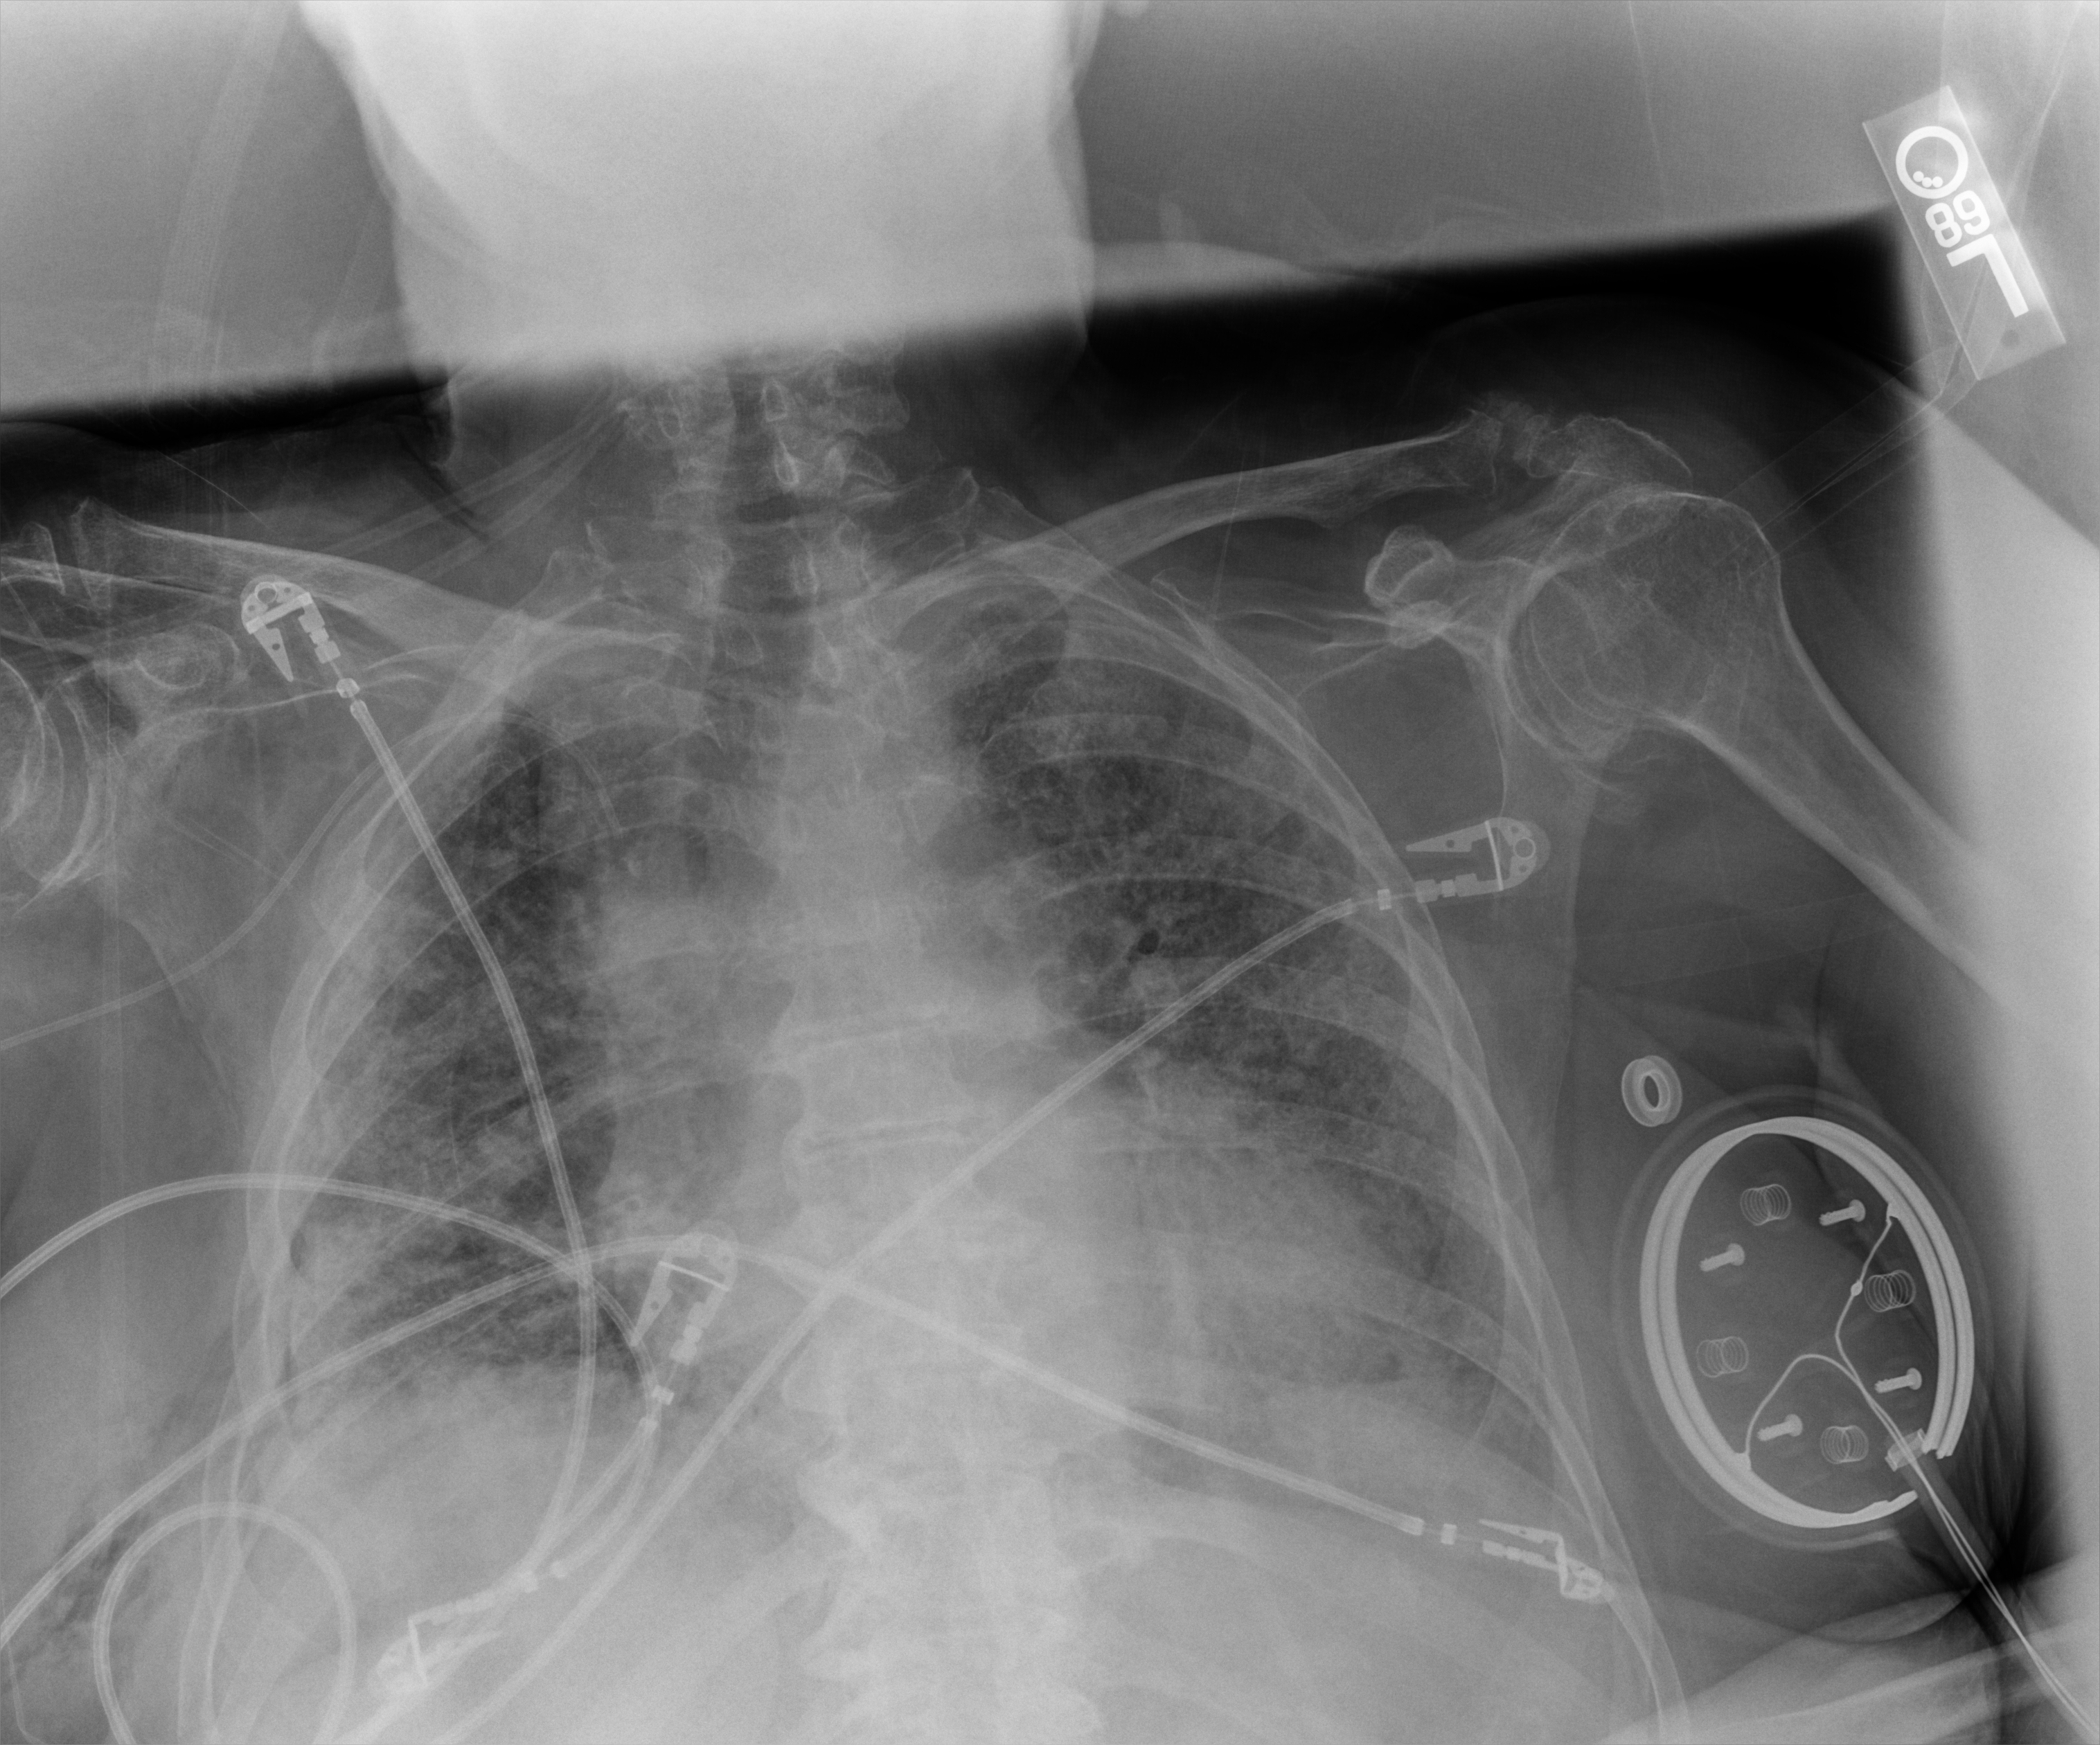
Bedside chest radiograph (digital radiography). Female patient hospitalised with COVID-19, age 75–90 years.
From the hospital-stay record, not from the radiograph (when in the stay this image was taken is not recorded):
- admitted to intensive care during this hospital stay: no
- other chronic lung disease (admission record): no
- hypertension (admission record): no